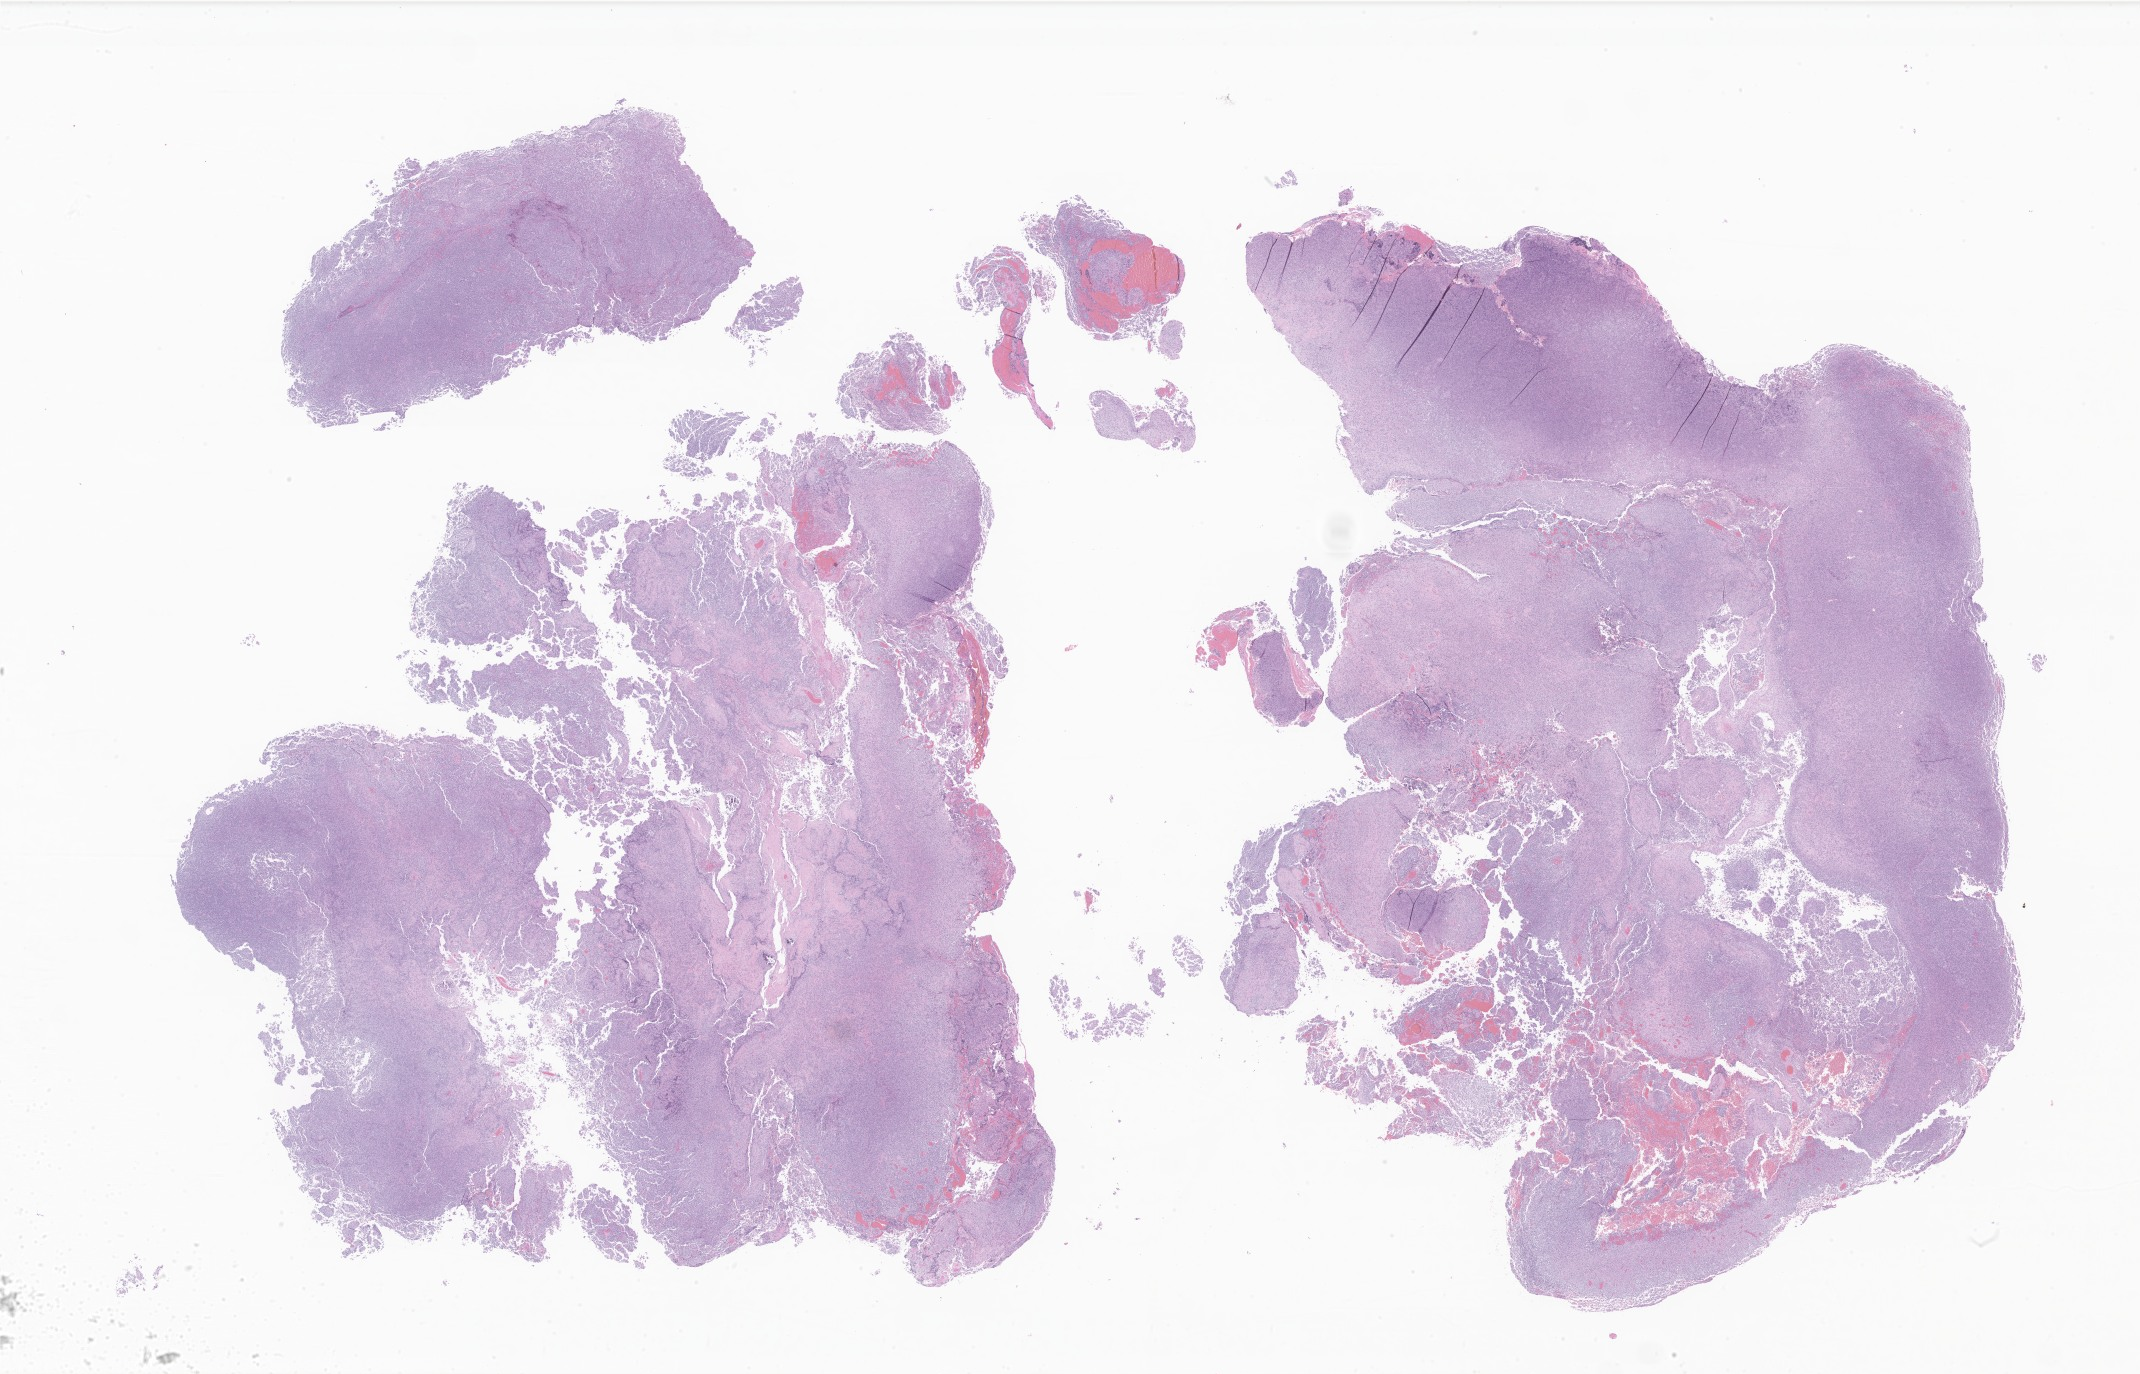
Hematoxylin and eosin (H&E) whole-slide image of tumor tissue from the brain, shown as a low-resolution overview of the whole scanned area (about 36.1 x 23.2 mm); FFPE section. Patient female; age 34 months (2 years 10 months).
* diagnosis: Ependymoma, NOS